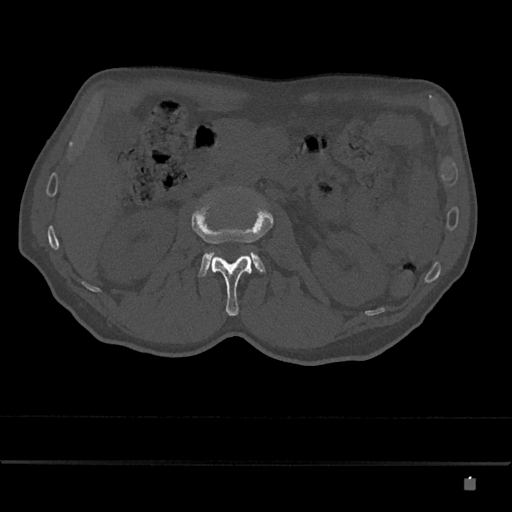
CT including the spine, one axial slice; slice 456 of 797 in the series (ordered by position); reconstruction kernel Br40s/3; 120 kVp; bone window (W 1800 / L 400 HU); 0.5 mm slice thickness; 512 × 512 image matrix, field of view 390 × 390 mm. Male patient, age 72 years. Case-level facts recorded for this patient, not image findings: primary cancer: prostate.
Annotated regions visible in this slice (semi-automatic segmentation, software-assisted and operator-edited):
- L2 vertebra: bounding box [x1, y1, x2, y2] px = [192, 206, 274, 316]
- L3 vertebra: [198, 252, 265, 277]